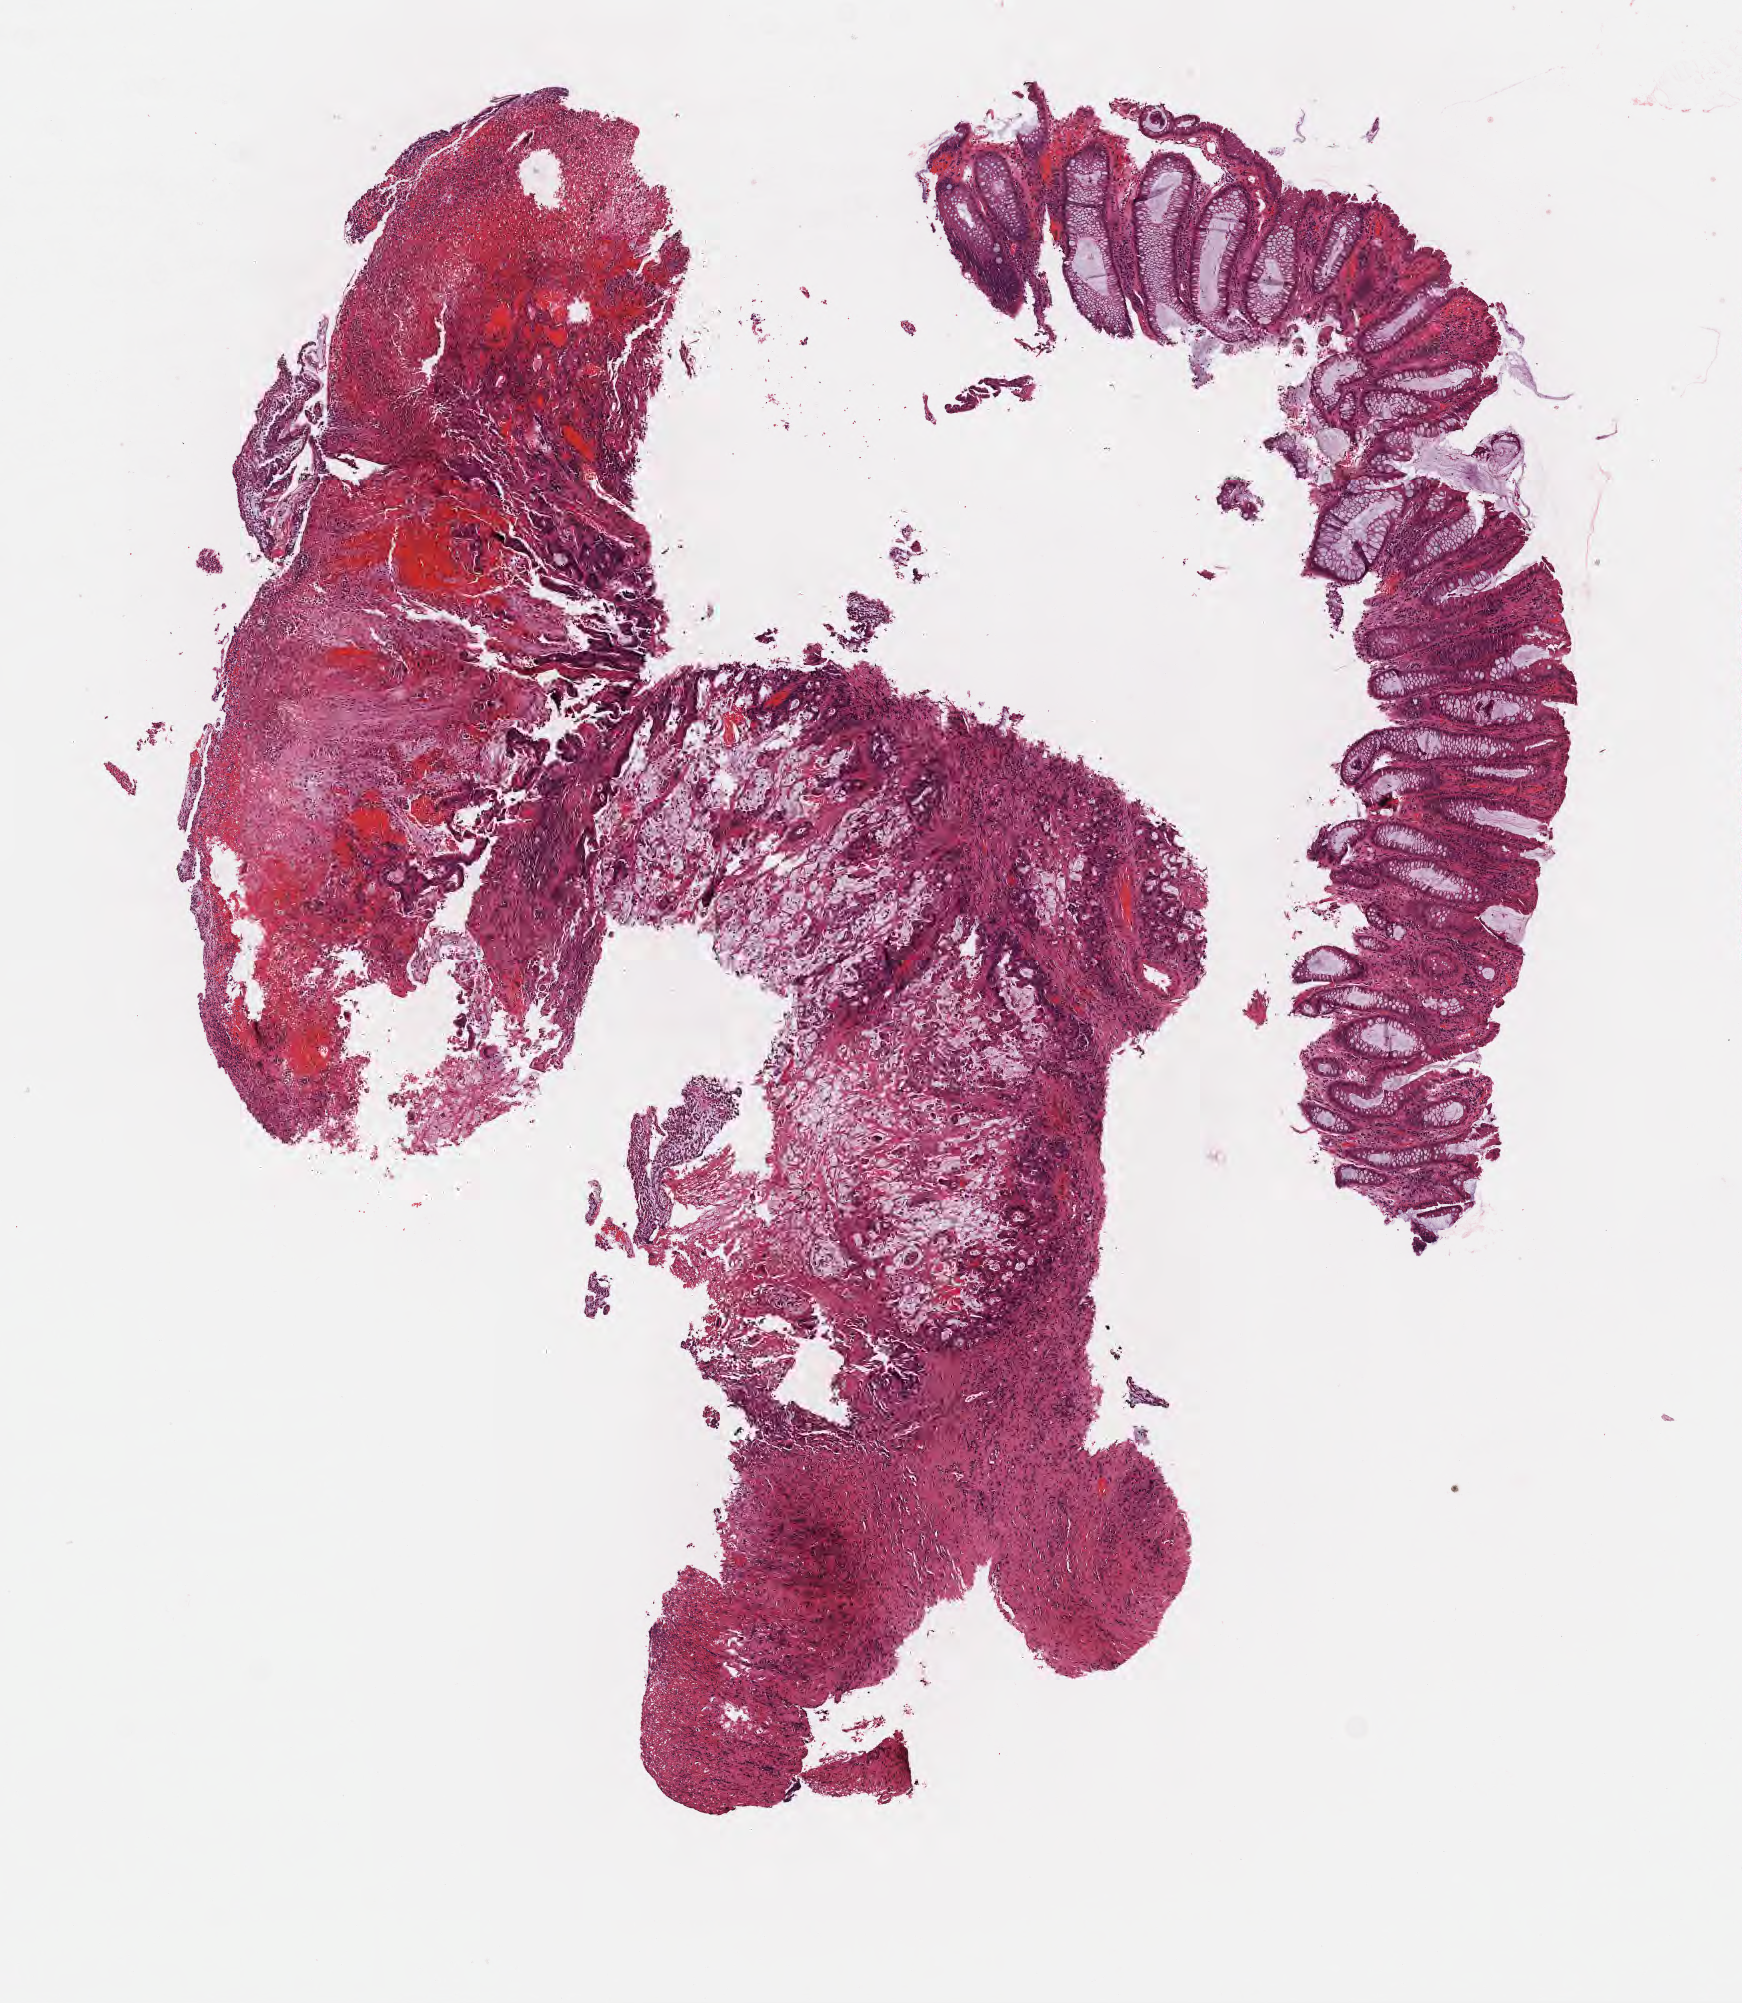
Whole-slide image, hematoxylin and eosin (H&E) stain, whole scanned area (about 7.0 x 8.1 mm) shown as a low-resolution overview. Formalin-fixed paraffin-embedded section. Specimen: primary tumor. Anatomic site: sigmoid colon. Male, age 55 years at initial diagnosis. Pathologist review of this section (percent, as recorded): tumor cells 75%, tumor nuclei 75%, stromal cells 19%, necrosis 0%, normal cells 6%. Inflammatory infiltration, as recorded: lymphocyte infiltration 5%, monocyte infiltration 1%, neutrophil infiltration 6%.
• section: top of the tissue portion
• histologic diagnosis: Mucinous adenocarcinoma
• AJCC pathologic stage: Stage IIIC